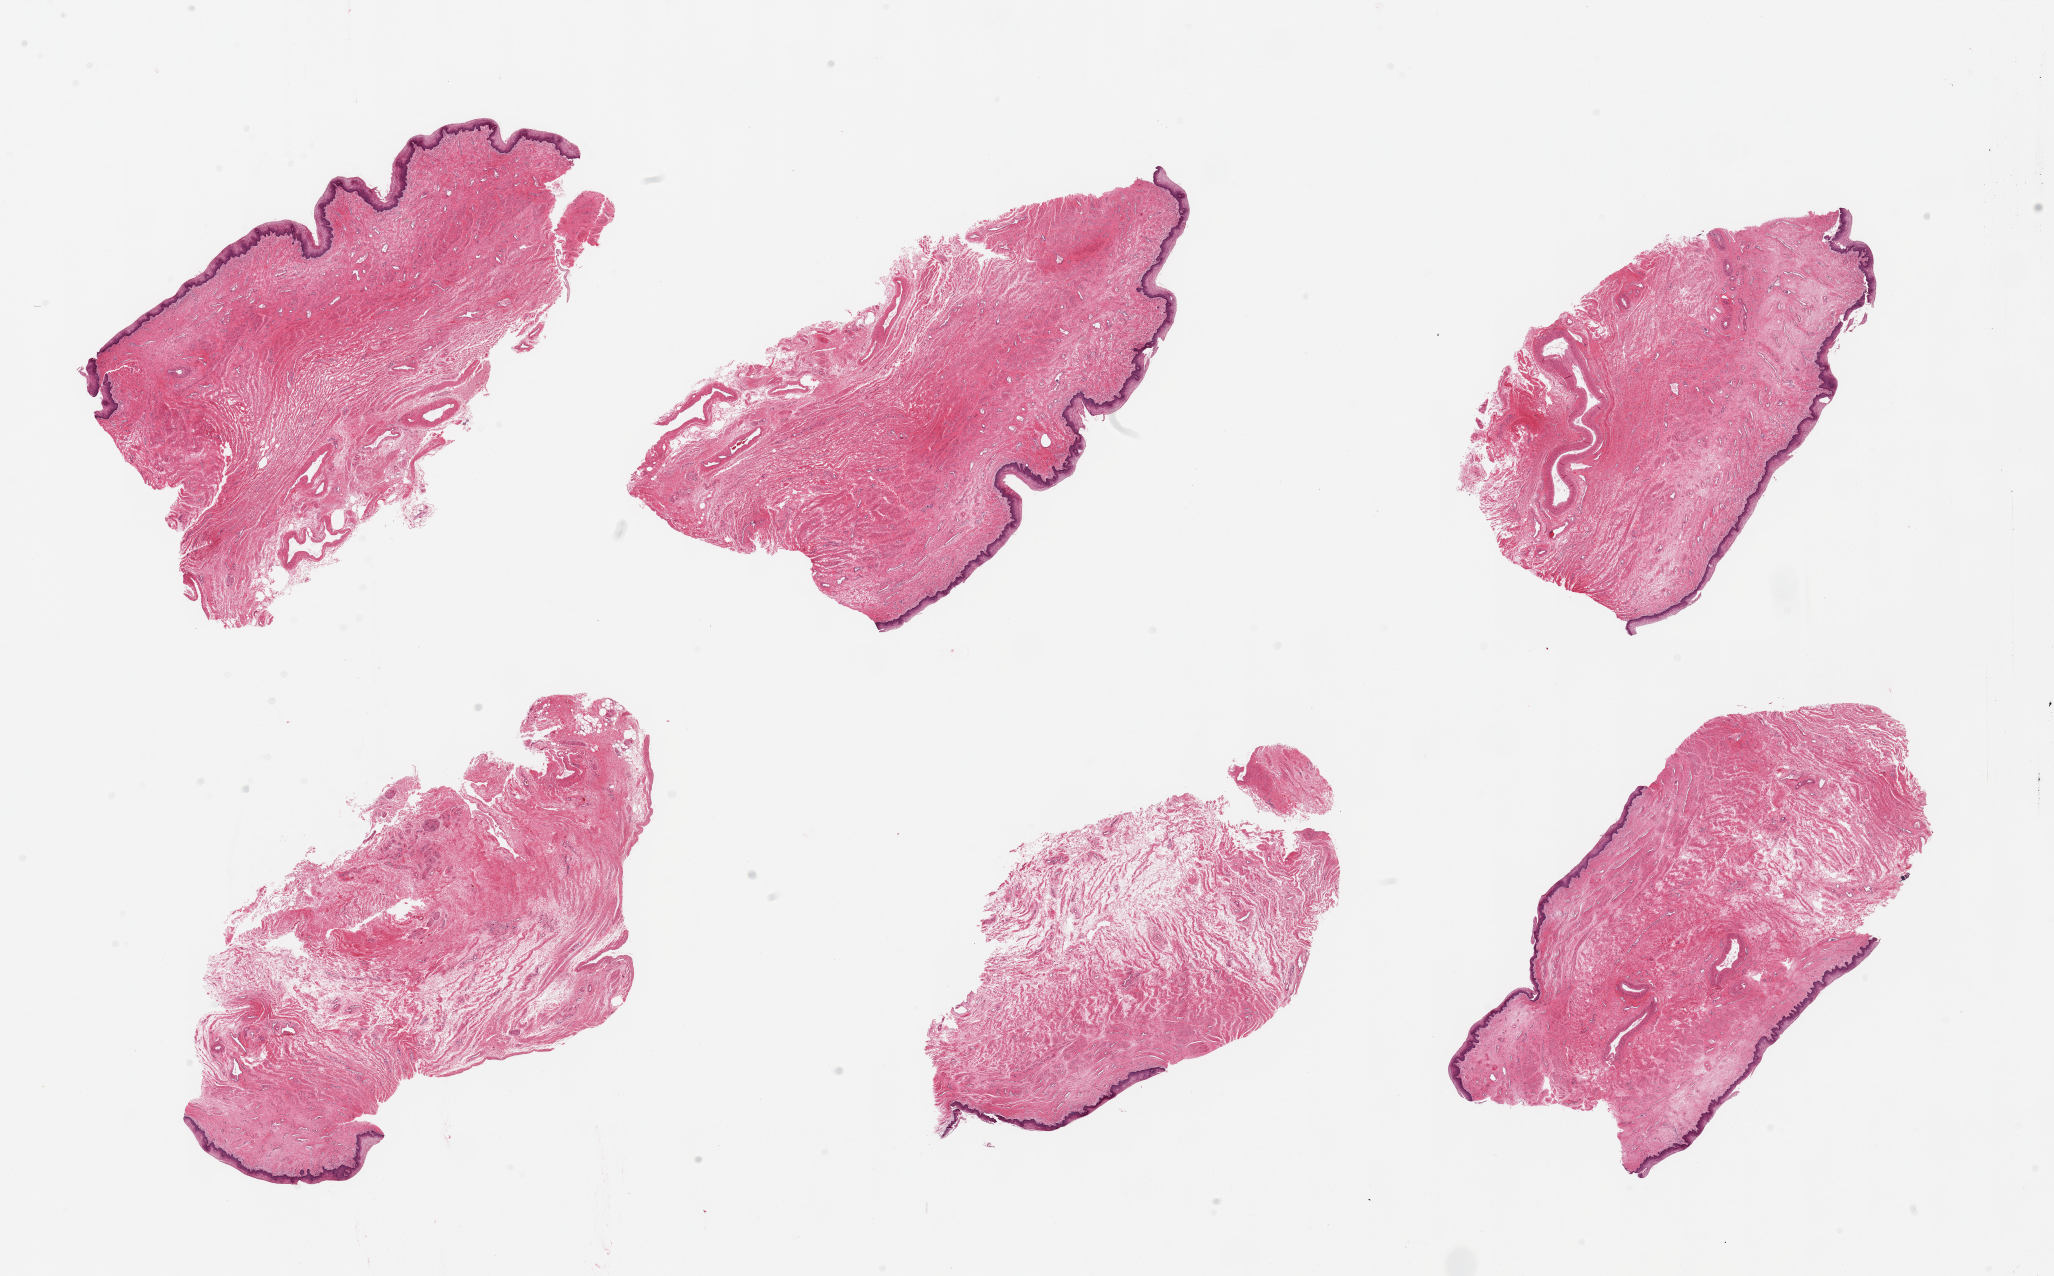
Whole-slide image, H&E stain — shown as a low-resolution overview of the whole scanned area (about 32.5 x 20.2 mm). PAXgene-fixed, paraffin-embedded tissue. Sampled site (target tissue): vagina. Donor tissue sample. Donor sex: female.
Reviewer comment on this tissue sample: 6 pieces.